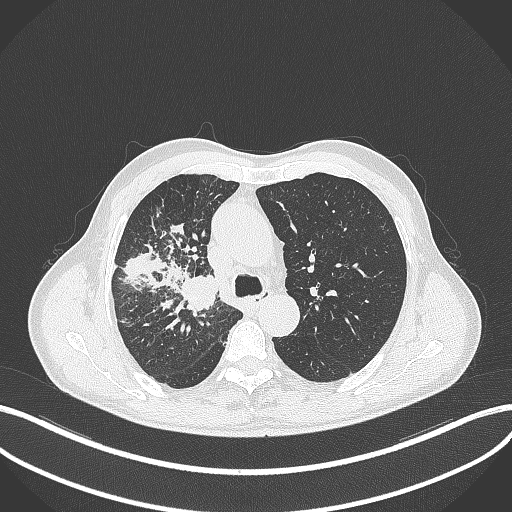
Chest CT, one axial slice; position 334 of 490 along the scan axis; reconstruction kernel B70f; lung window (W 1500 / L -600 HU); 512 × 512 image matrix, field of view 400 × 400 mm. Male patient, age 69 years. From the clinical record (not read from this slice): clinical TNM (as recorded): T2a N0 M0.
Outlined on this slice (bounding box drawn by a radiologist):
- lung tumour (recorded histology: adenocarcinoma): bounding box [x1, y1, x2, y2] px = [176, 272, 223, 311]